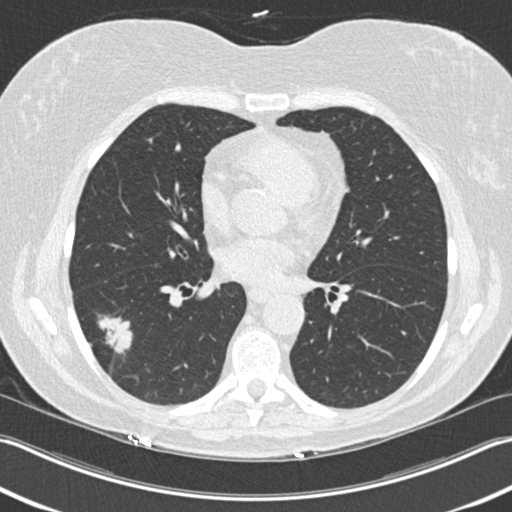
Low-dose screening chest CT, axial slice, first (baseline) screen, lung window (W 1500 / L -600 HU). Female participant, aged 63 years at enrolment. Current smoker at enrolment.
Expert-annotated lung lesion, bounding box (x1, y1, x2, y2) in pixels: (73, 312, 136, 371). The screening reader recorded 3 non-calcified nodules or masses ≥4 mm on this exam; which of them this box marks is not recorded. Participant outcome: lung cancer diagnosed 57 days after this screen — bronchiolo-alveolar adenocarcinoma, NOS, right lower lobe, well differentiated (G1), stage IA (AJCC 6th edition), 25 mm at pathology.